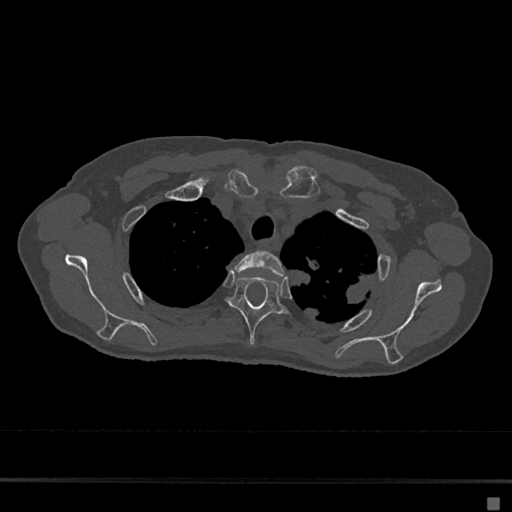
CT including the spine, one axial slice. Reconstruction kernel Br40s/3. Bone window (W 1800 / L 400 HU). 0.5 mm slice thickness. 512 × 512 image matrix, field of view 360 × 360 mm. Female patient, age 68 years. From the clinical record (not read from this slice): primary cancer: renal.
Outlined on this slice (semi-automatically segmented with operator editing):
- T2 vertebra: bounding box <234,251,284,276> (left, top, right, bottom; pixels)
- T3 vertebra: <228,276,287,346>